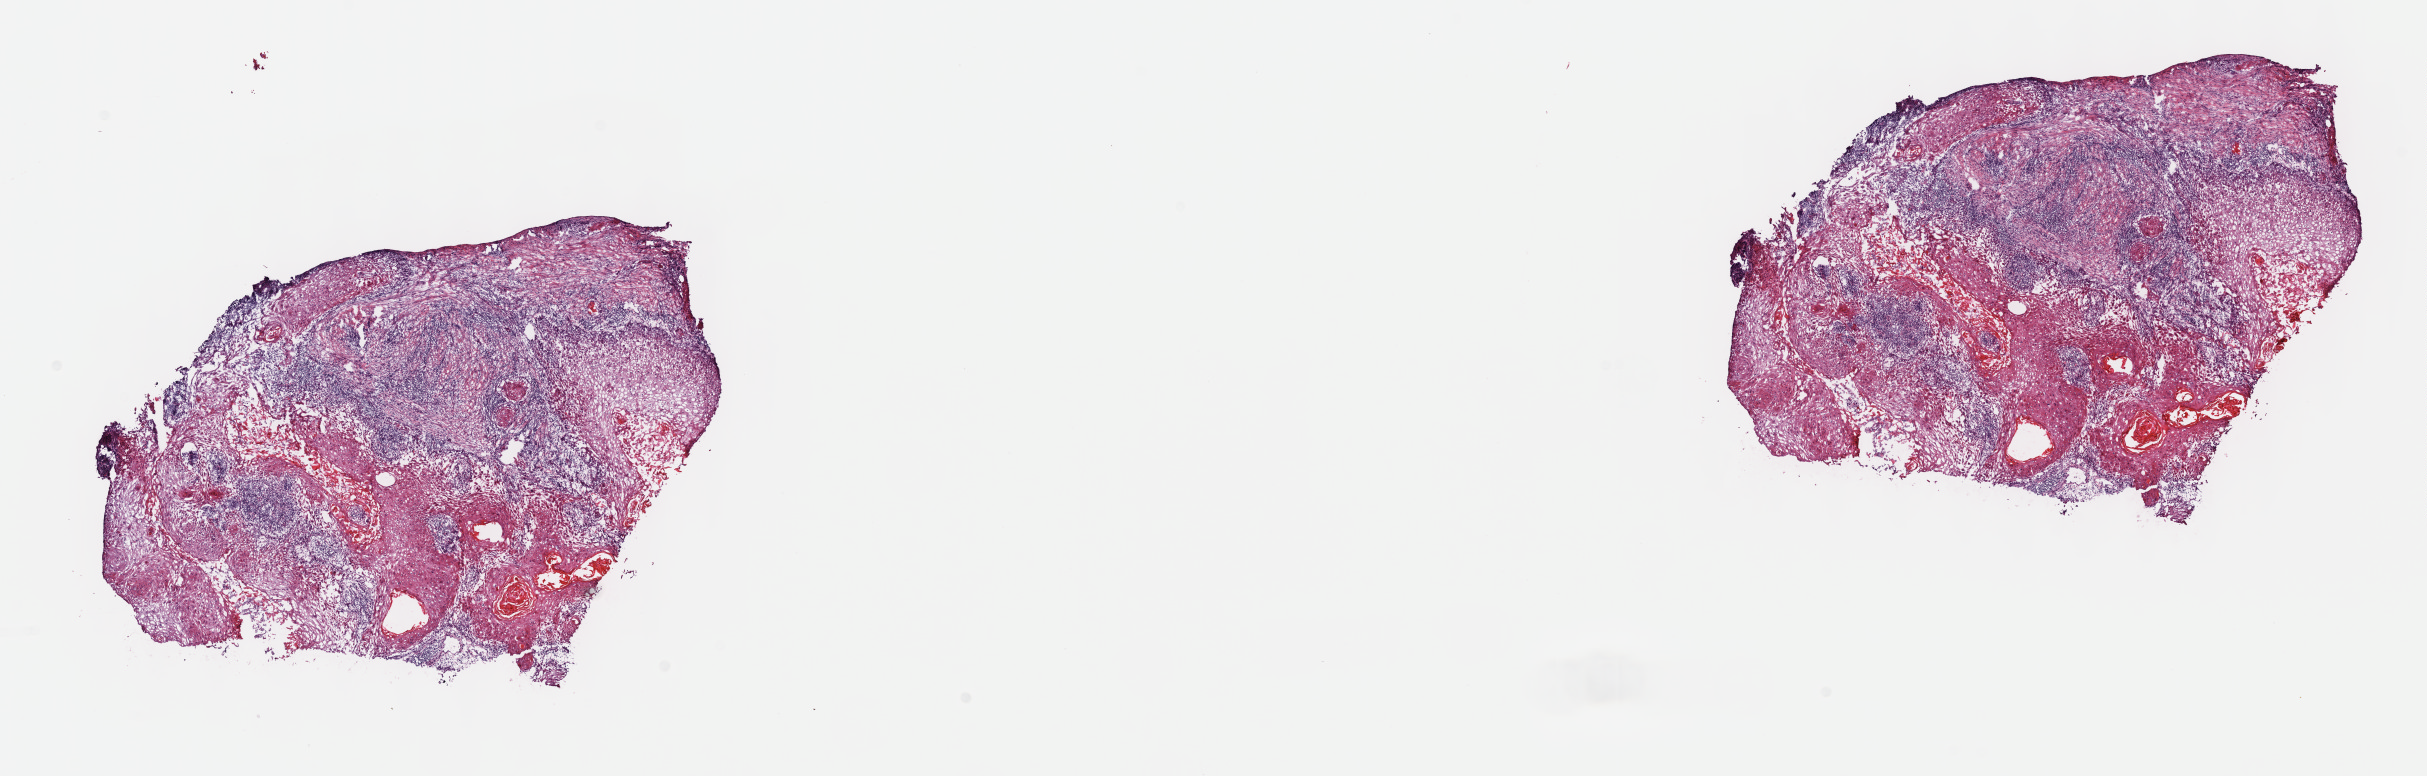
H&E-stained whole-slide image, whole scanned area (about 19.6 x 6.3 mm) shown as a low-resolution overview; frozen section from the top of the tissue portion; sample: primary tumour, head and neck. Patient: male, age at initial diagnosis 68 years.
Diagnosis: Squamous cell carcinoma, keratinizing, NOS (larynx, NOS).